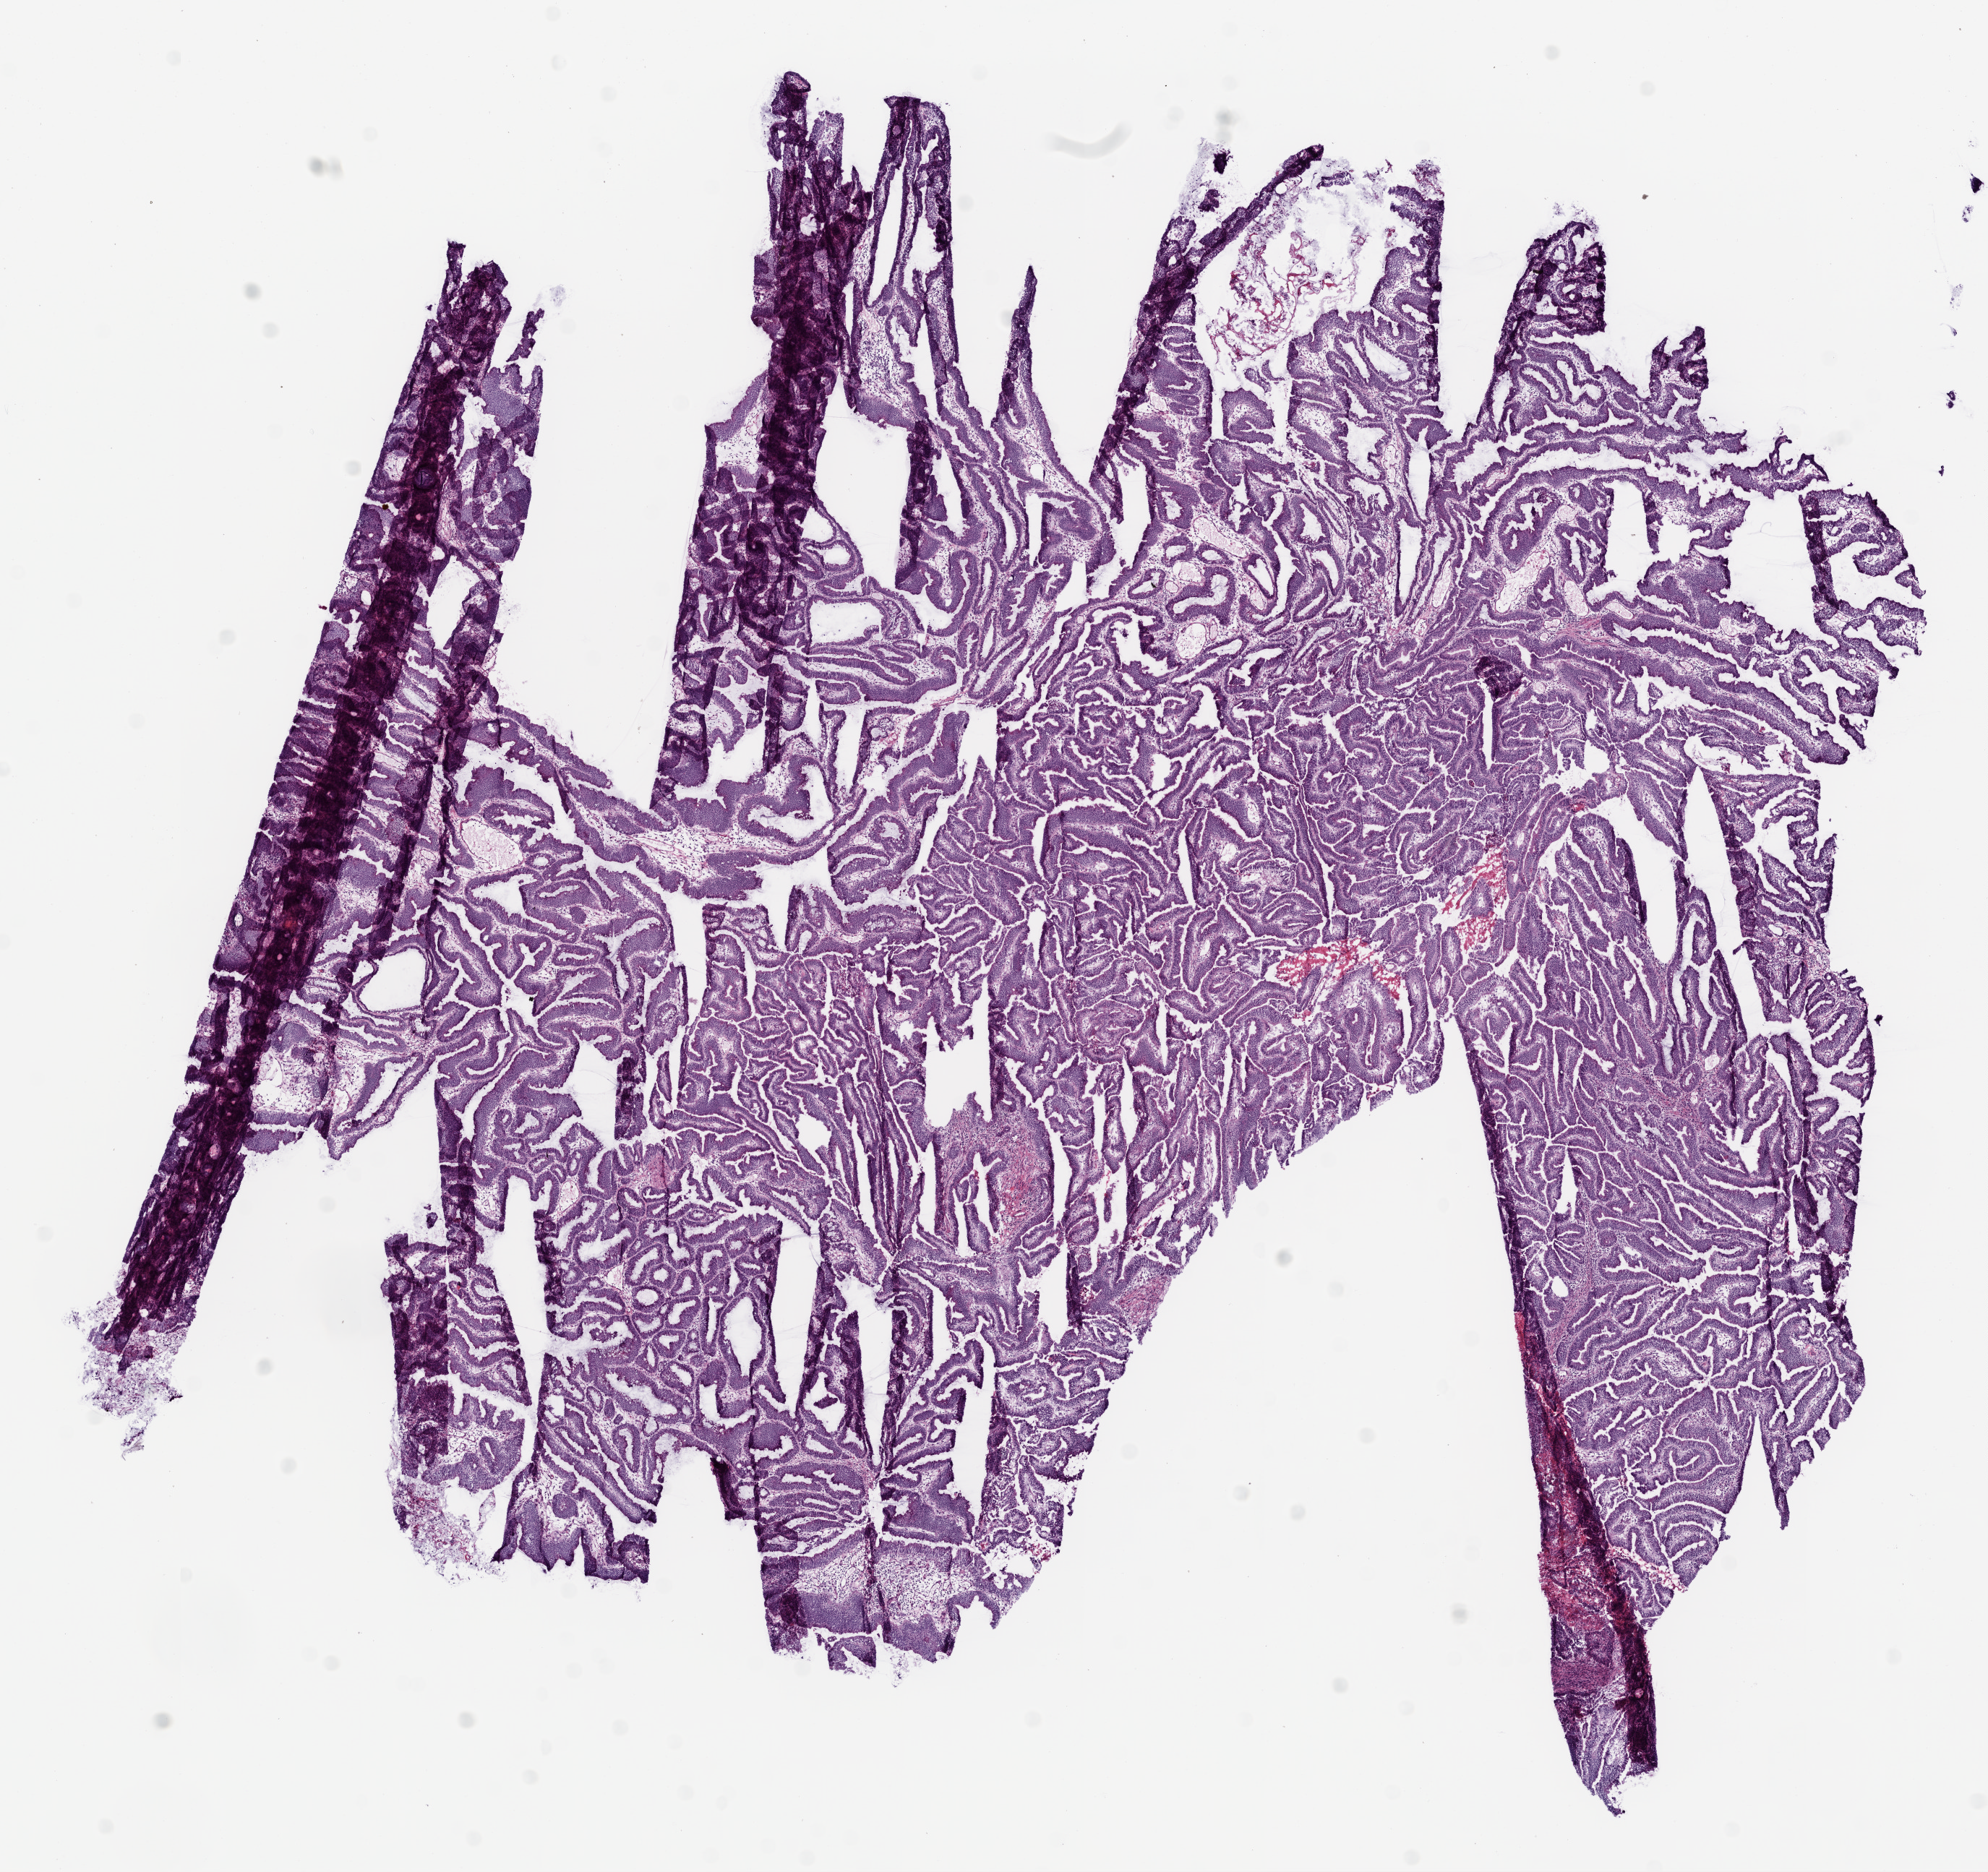
Hematoxylin and eosin (H&E) stained whole-slide image — low-resolution overview of the scanned area, about 11.0 x 10.4 mm (acquisition: 20x scan); frozen section from the bottom of the tissue portion; sample: primary tumour, stomach. Female patient; age at initial diagnosis 71 years. Composition of this section per pathologist review: tumour cells 87%, tumour nuclei 85%.
Pathologic diagnosis: Adenocarcinoma, NOS (body of stomach).